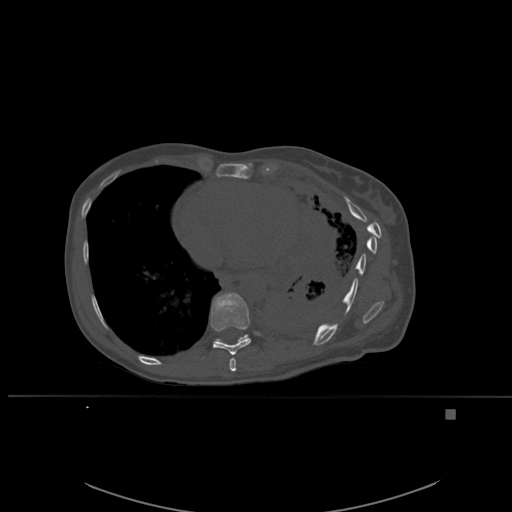
CT including the spine, one axial slice. Slice 332 of 537 in the series (ordered by position). Bone window (W 1800 / L 400 HU). 1.5 mm slice thickness. 512 × 512 image matrix, field of view 440 × 440 mm. Patient: female, 45 years. From the clinical record (not read from this slice): primary cancer: lung.
Annotated regions visible in this slice (semi-automatic segmentation, software-assisted and operator-edited):
- T10 vertebra: box from (x=237, y=334) to (x=248, y=343) px
- T8 vertebra: (x=229, y=358)–(x=237, y=372)
- T9 vertebra: (x=211, y=293)–(x=251, y=356)